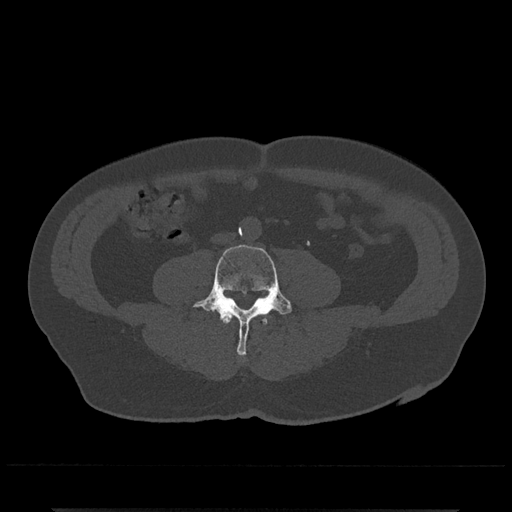
CT including the spine, one axial slice; slice 153 of 797 in the series (ordered by position); reconstruction kernel Br40s/3; bone window (W 1800 / L 400 HU); 0.5 mm slice thickness; 512 × 512 image matrix. Male patient, age 67 years. From the clinical record (not read from this slice): primary cancer: prostate.
Annotated regions visible in this slice (semi-automatic segmentation, software-assisted and operator-edited):
- L3 vertebra: bounding box (x1, y1, x2, y2) in pixels: (221, 315, 268, 325)
- L4 vertebra: (192, 244, 292, 356)